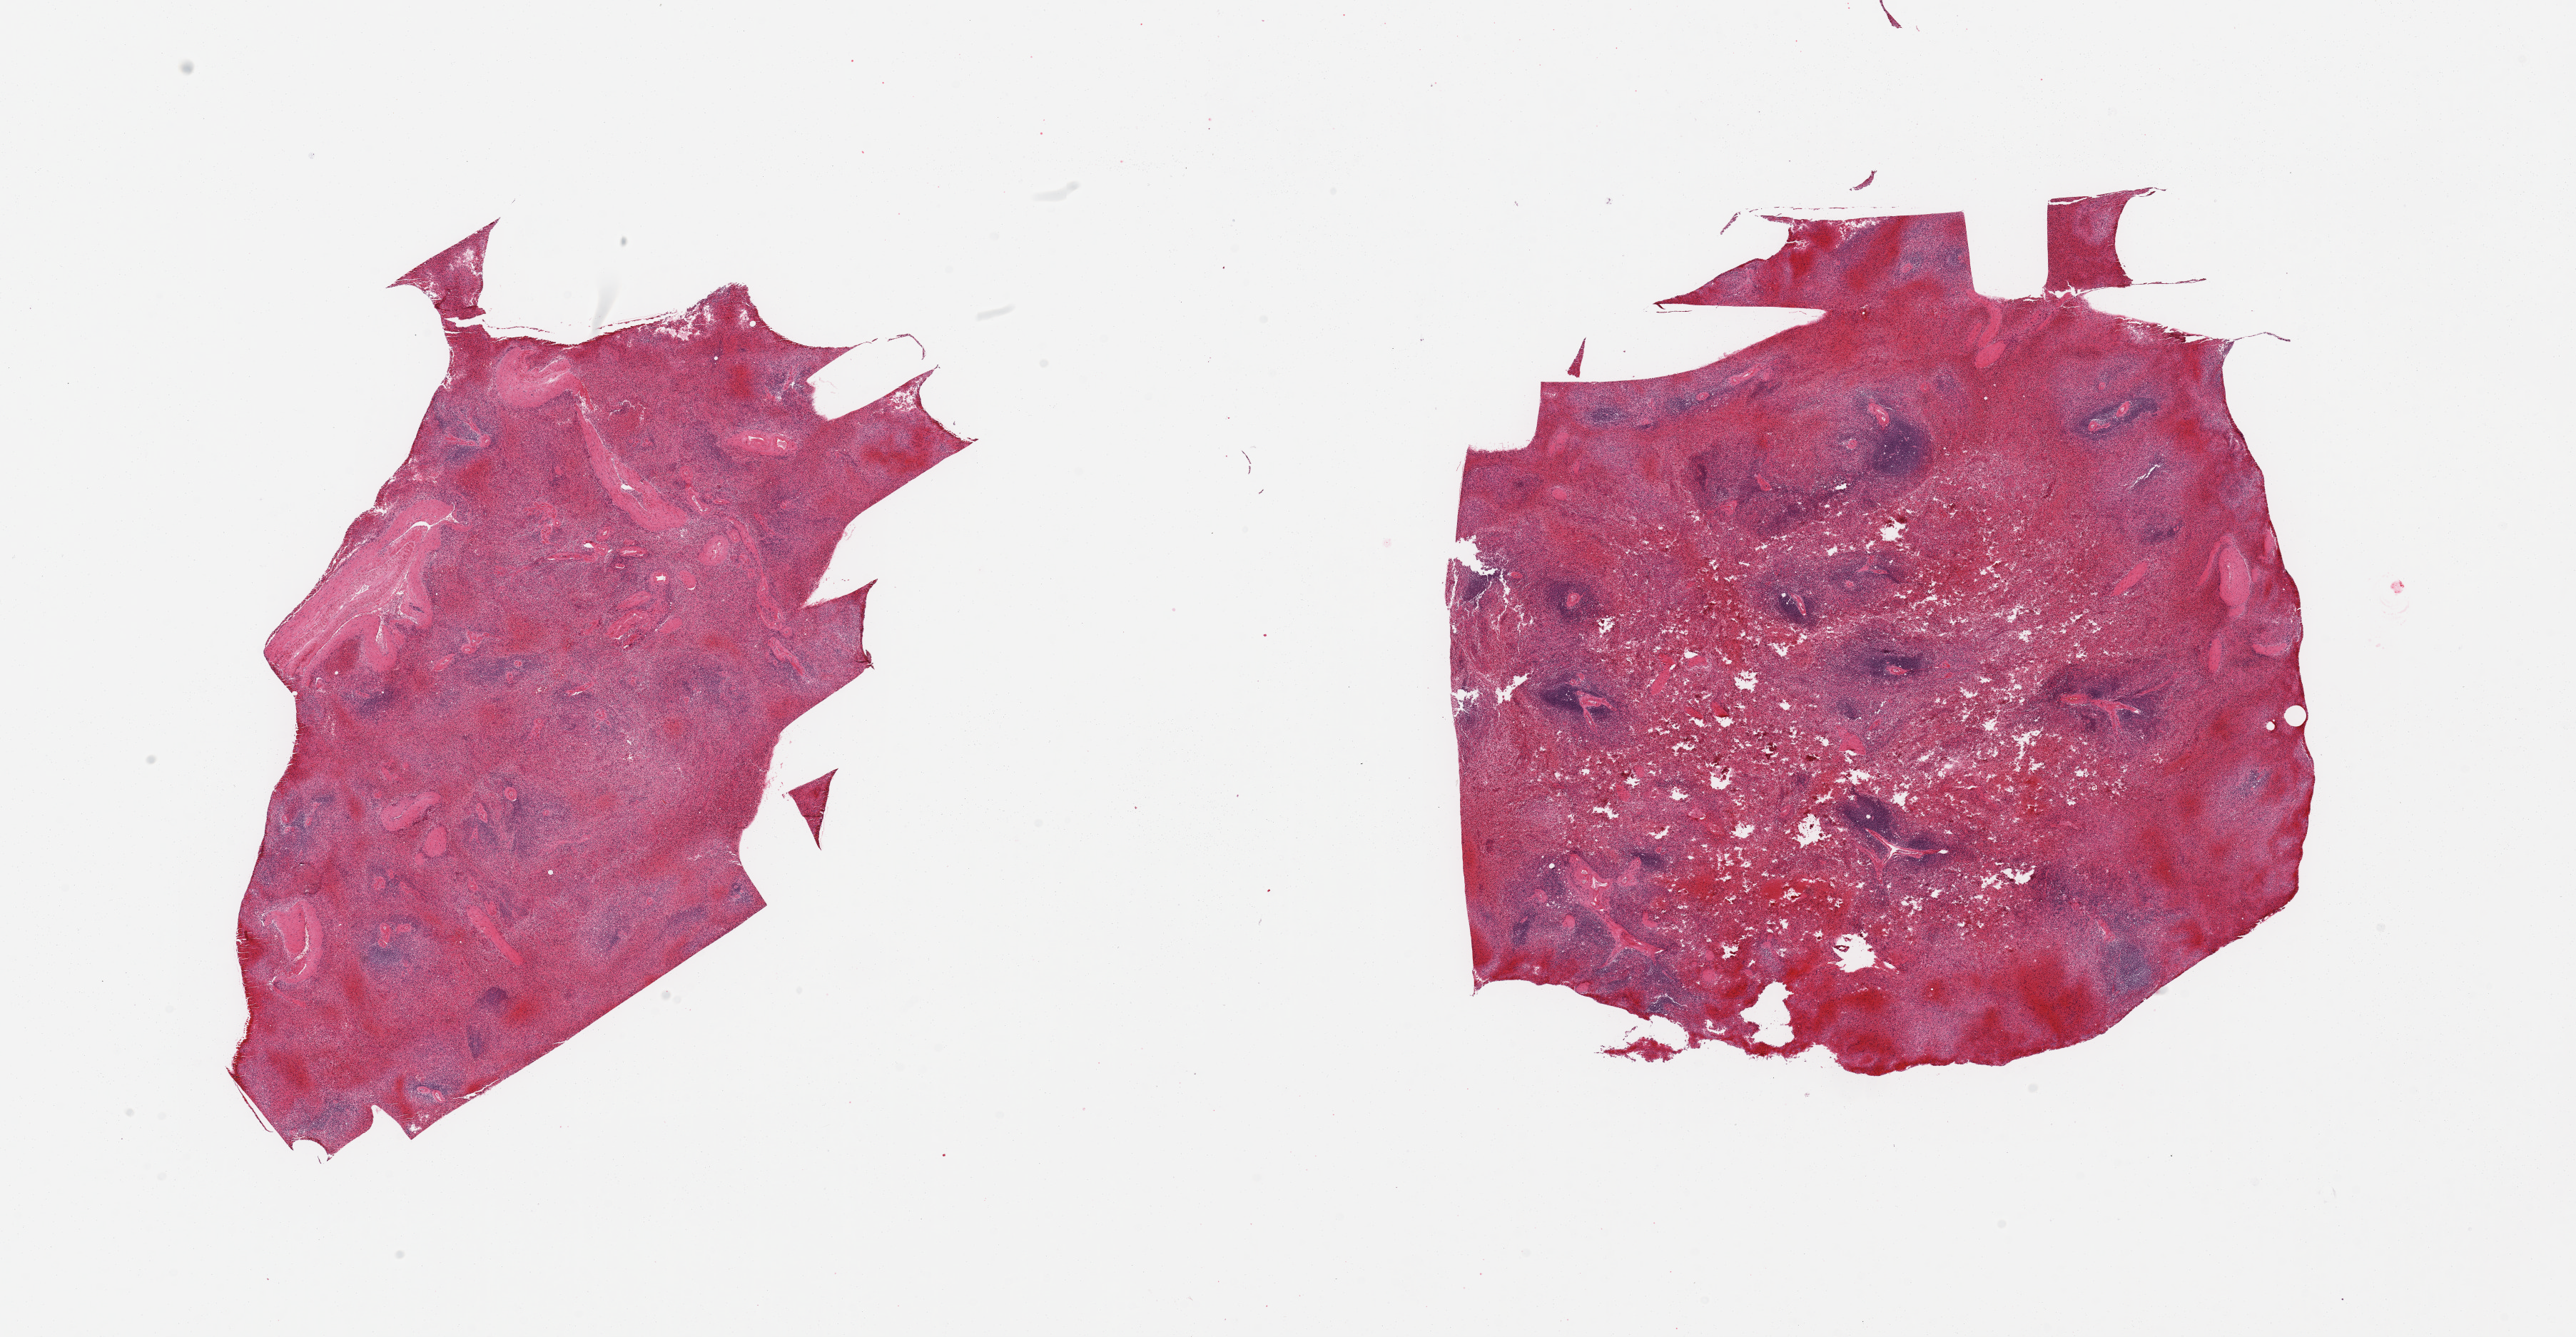
Haematoxylin and eosin whole-slide image, whole scanned area (about 28.5 x 14.8 mm, slide scanned at 20x) shown as a low-resolution overview, PAXgene-fixed paraffin-embedded (PFPE) section, target tissue: spleen, tissue donor sample. Donor: male.
Pathologist's review note for this sample: 2 pieces; congested.